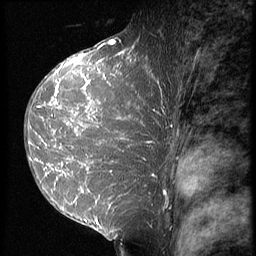
Breast MRI (dynamic contrast-enhanced), one sagittal slice. Slice 38 of 64 in the series (ordered by position). 3 images stored at this slice position (order not interpretable as contrast timing). 1.5 T. TE 4.2 ms, TR 9 ms. 256 × 256 image matrix. Female patient, age 39 years. Case-level facts recorded for this patient, not image findings: setting: breast cancer imaged before/during neoadjuvant chemotherapy; receptor status: HER2-positive.
Outlined on this slice (semi-automatic segmentation, software-assisted and operator-edited):
- analysis volume of interest (the breast-tissue region the enhancement analysis was run in; not a lesion): box from (x=24, y=47) to (x=159, y=239) px
- tumour enhancement mask (voxels above the 140 % enhancement threshold inside the analysis volume of interest): (x=30, y=47)–(x=154, y=210)